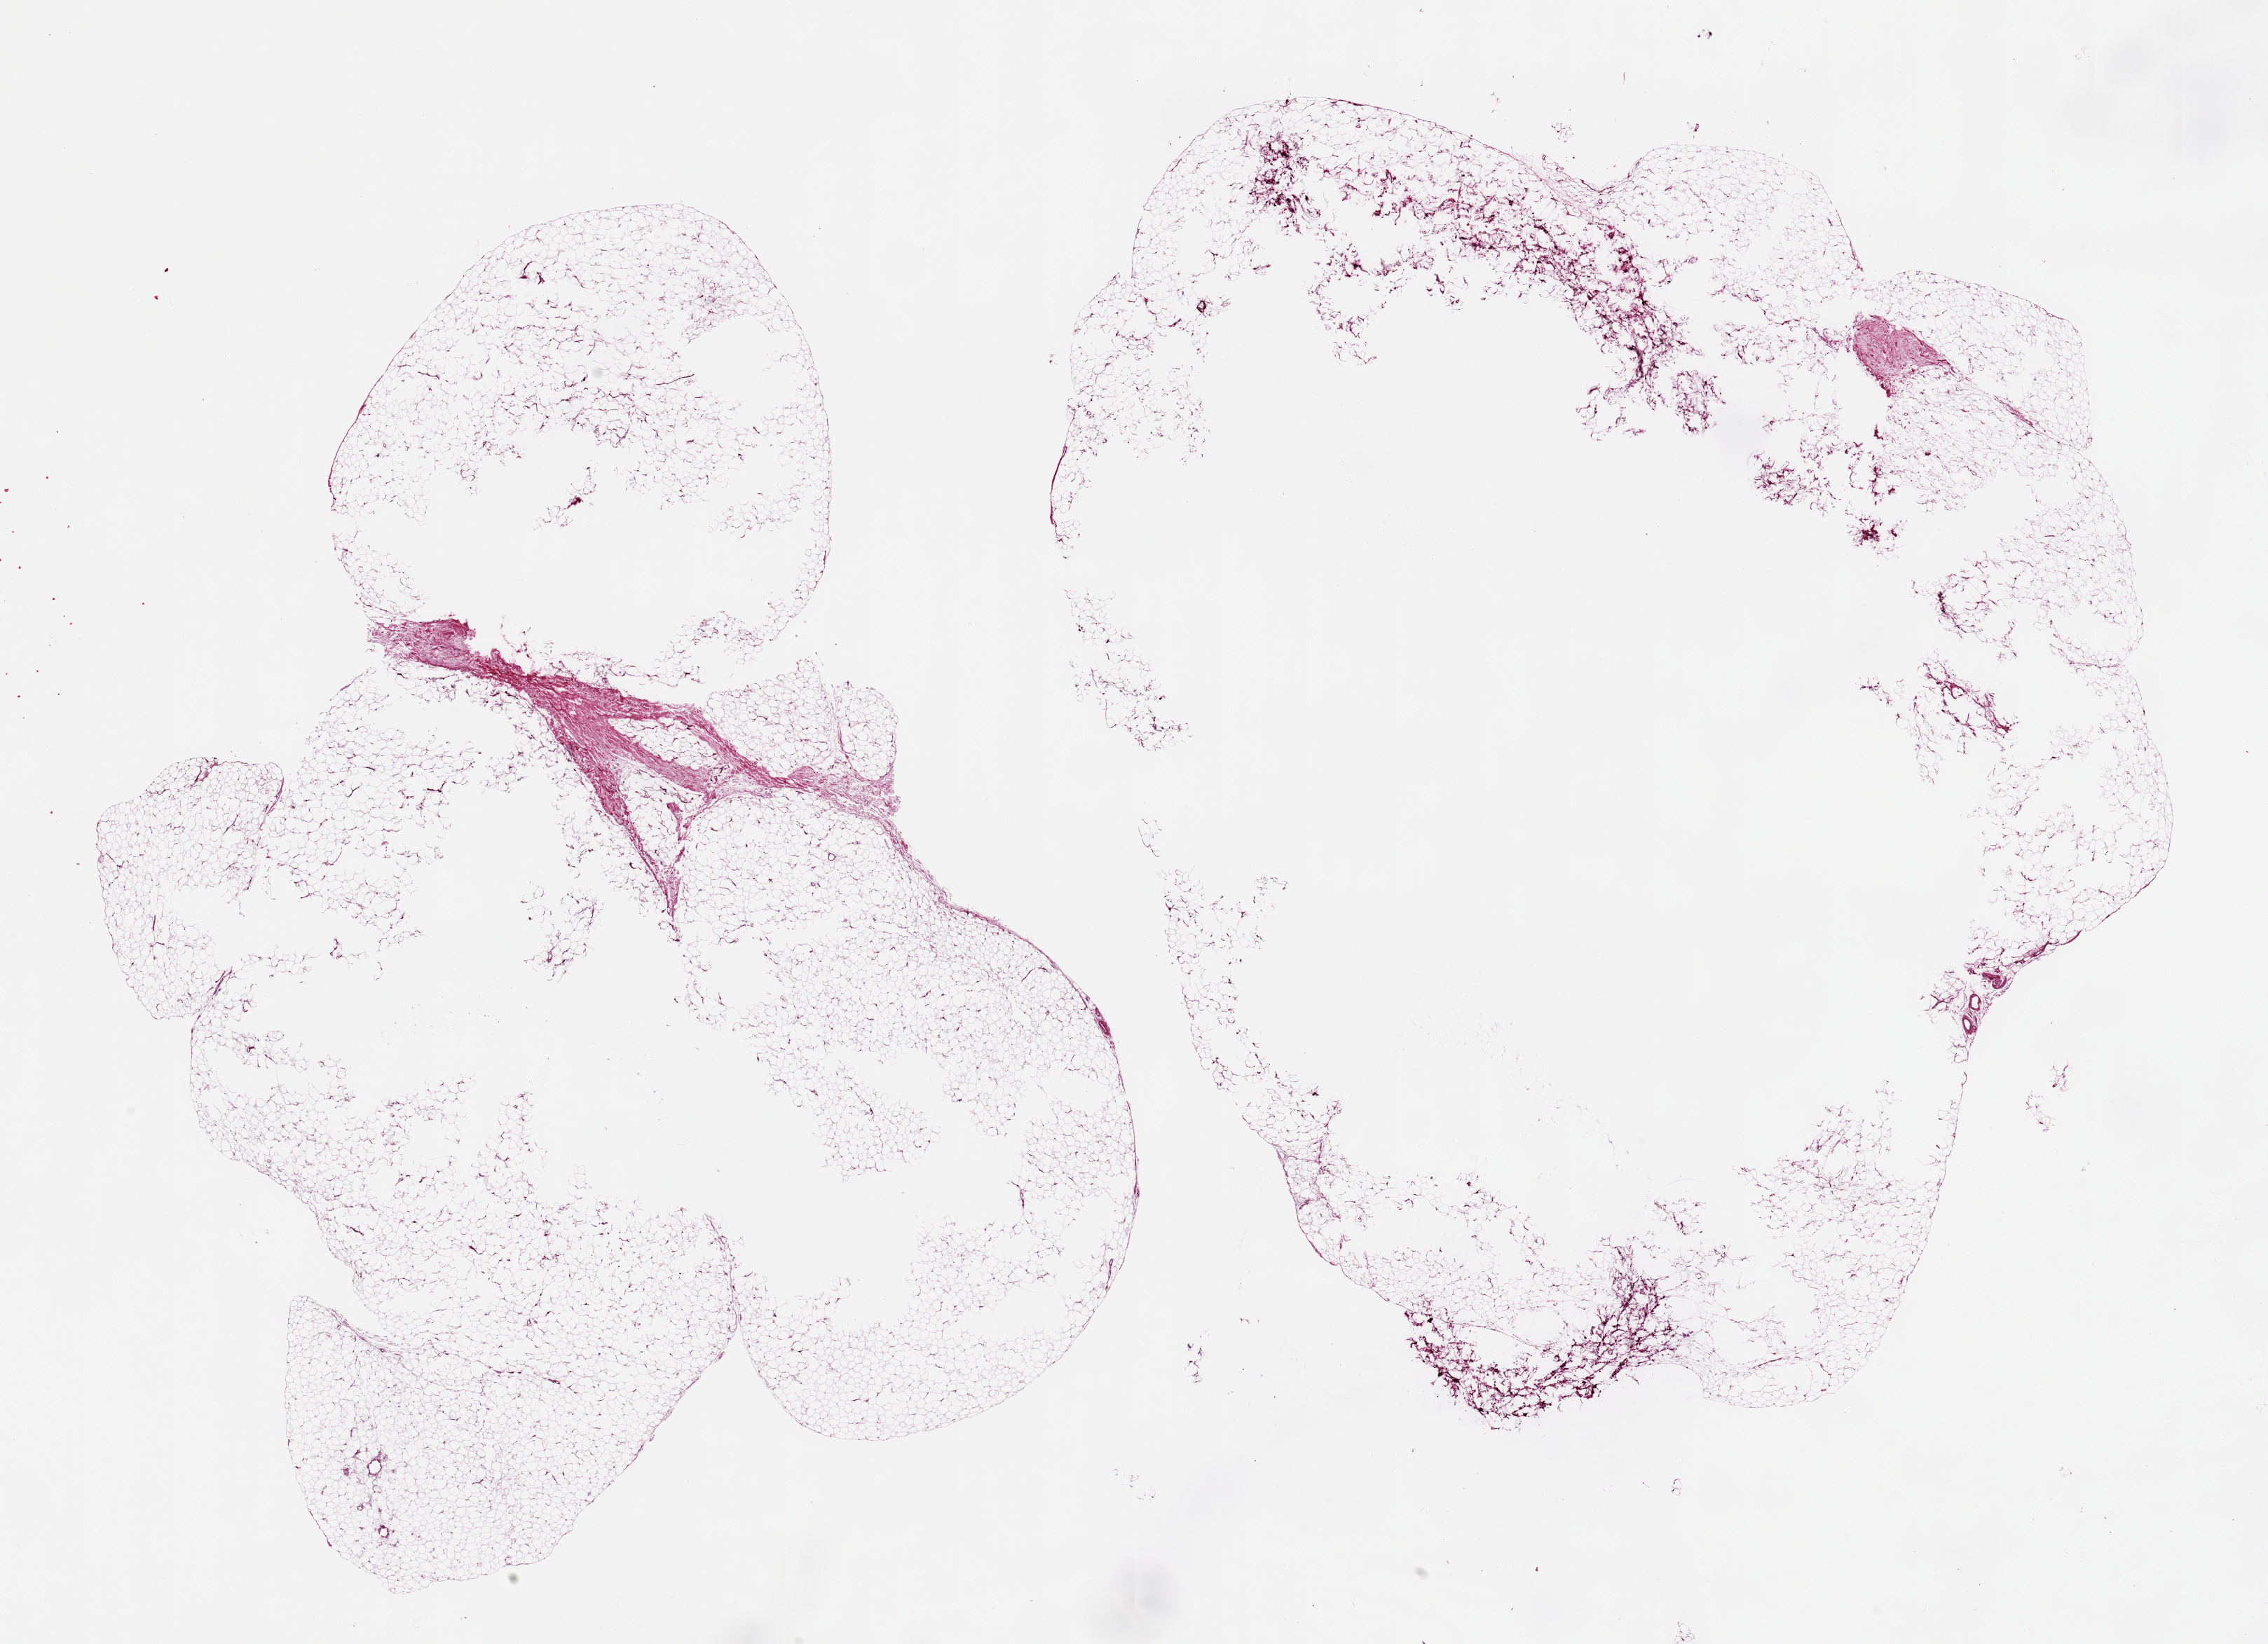
Hematoxylin and eosin (H&E) whole-slide image, low-resolution overview of the scanned area, about 25.6 x 18.6 mm; PAXgene-fixed paraffin-embedded (PFPE) section; section of adipose tissue (target tissue); donor tissue sample.
- reviewer comment on this tissue sample: 2 pieces 15x13 & 13x10 mm; excessively large aliquots with large central unfixed holes